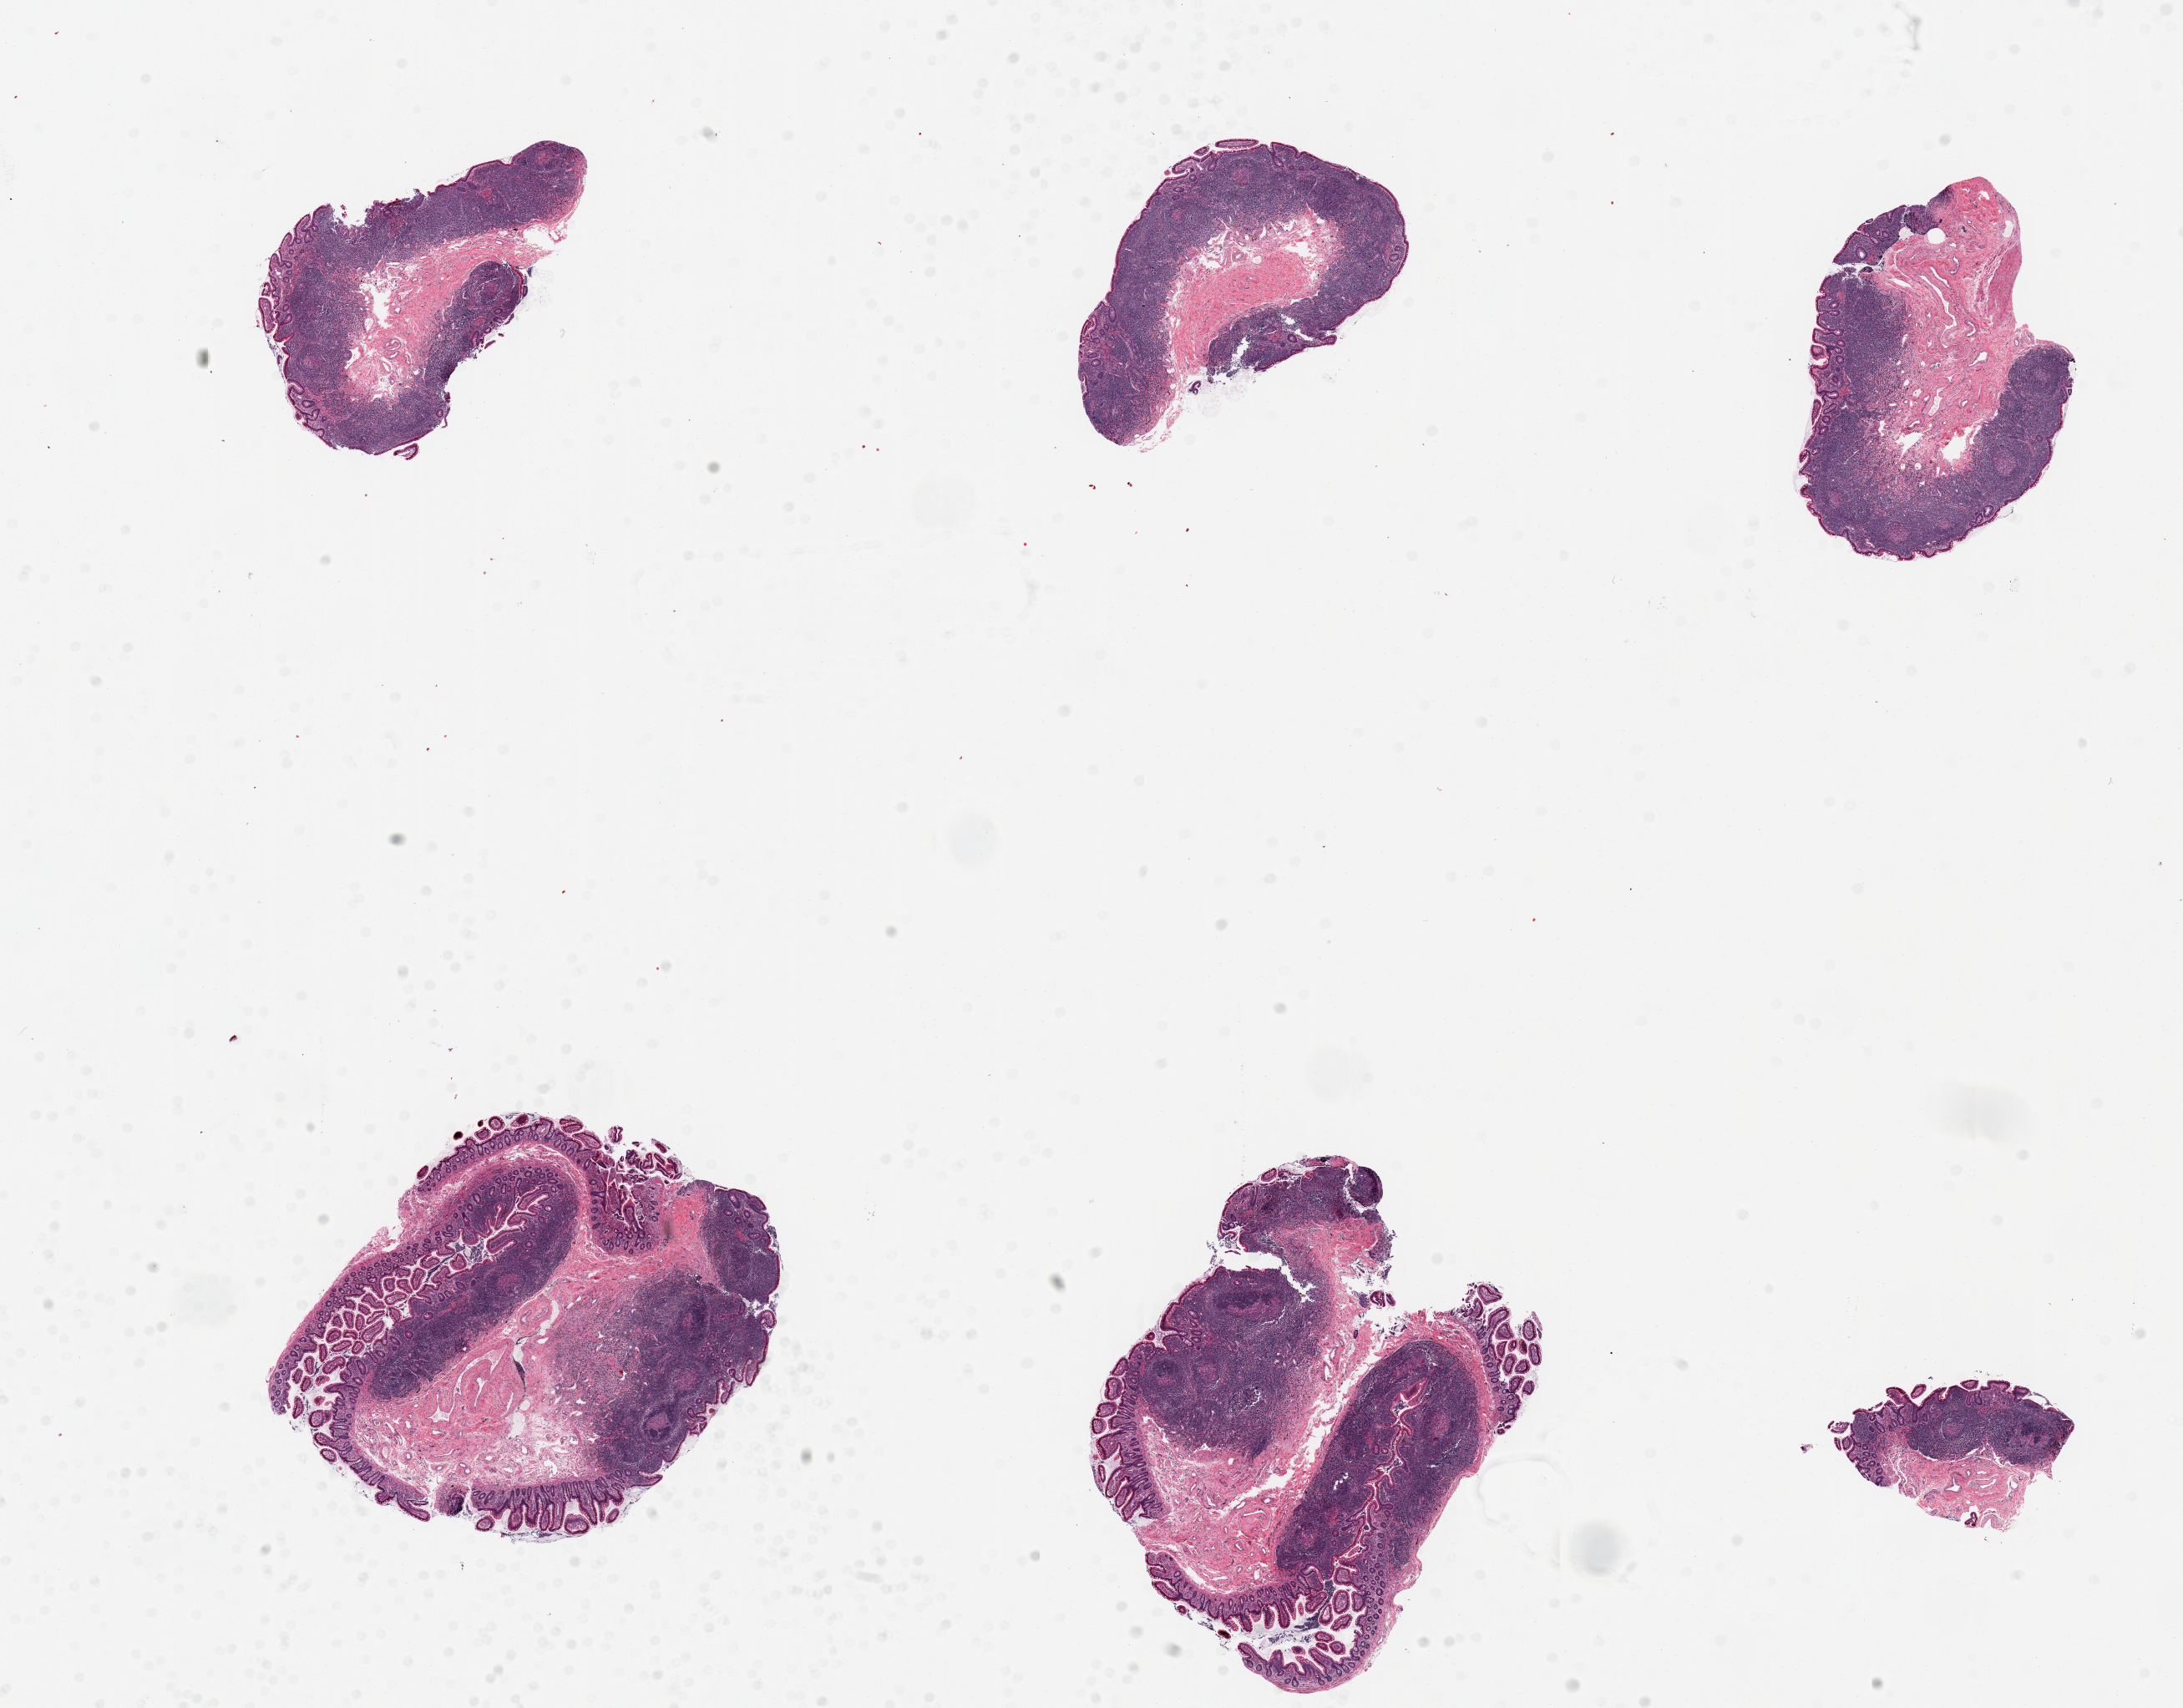
Whole-slide image, haematoxylin and eosin stain — low-resolution overview of the scanned area, about 20.7 x 16.2 mm (slide scanned at 20x), PAXgene-fixed paraffin-embedded (PFPE) section, target tissue: ileum, tissue donor sample. Donor: female.
Pathologist's review note for this sample: 6 pieces, well trimmed and well preserved with prominent lymphoid tissue.